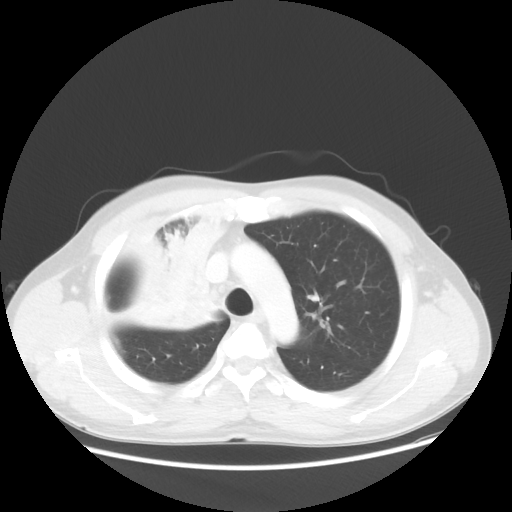
Chest CT, one axial slice; position 40 of 56 along the scan axis; 100 kVp; lung window (W 1500 / L -600 HU); 5 mm slice thickness; 512 × 512 image matrix, field of view 398 × 398 mm. Patient: male, 60 years. Case-level facts recorded for this patient, not image findings: clinical TNM (as recorded): T2a N1 M0.
Structures marked on this image (bounding box drawn by a radiologist):
- lung tumour (recorded histology: squamous cell carcinoma): bounding box (x1, y1, x2, y2) in pixels: (113, 194, 247, 352)